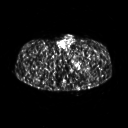
FDG PET of an extremity soft-tissue mass (from a PET/CT study), one axial slice. Slice 264 of 267 in the series (ordered by position). 3.27 mm slice thickness. 128 × 128 image matrix, field of view 500 × 500 mm. Male patient, age 27 years. Case-level facts recorded for this patient, not image findings: histological type: extraskeletal osteosarcoma; grade: high; site of the primary tumour: left adductur.
Annotated regions visible in this slice (expert contour drawn on MRI and transferred to this co-registered scan by the dataset authors):
- gross tumour volume (mass): bounding box [x1, y1, x2, y2] px = [70, 49, 97, 75]